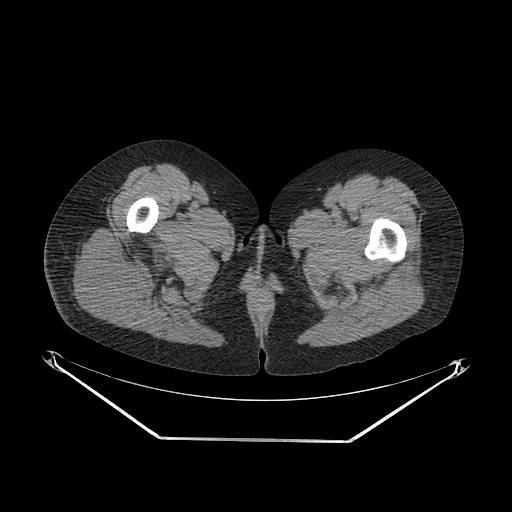
CT of an extremity soft-tissue mass (from a PET/CT study), one axial slice. Position 29 of 267 along the scan axis. Soft-tissue window (W 400 / L 40 HU). 3.75 mm slice thickness. 512 × 512 image matrix, field of view 500 × 500 mm. Female patient. Case-level facts recorded for this patient, not image findings: histological type: epithelioid sarcoma with vascular differentiation; site of the primary tumour: right buttock.
Annotated regions visible in this slice (expert contour drawn on MRI and transferred to this co-registered scan by the dataset authors):
- gross tumour volume (mass): bounding box (x1, y1, x2, y2) in pixels: (73, 233, 147, 316)